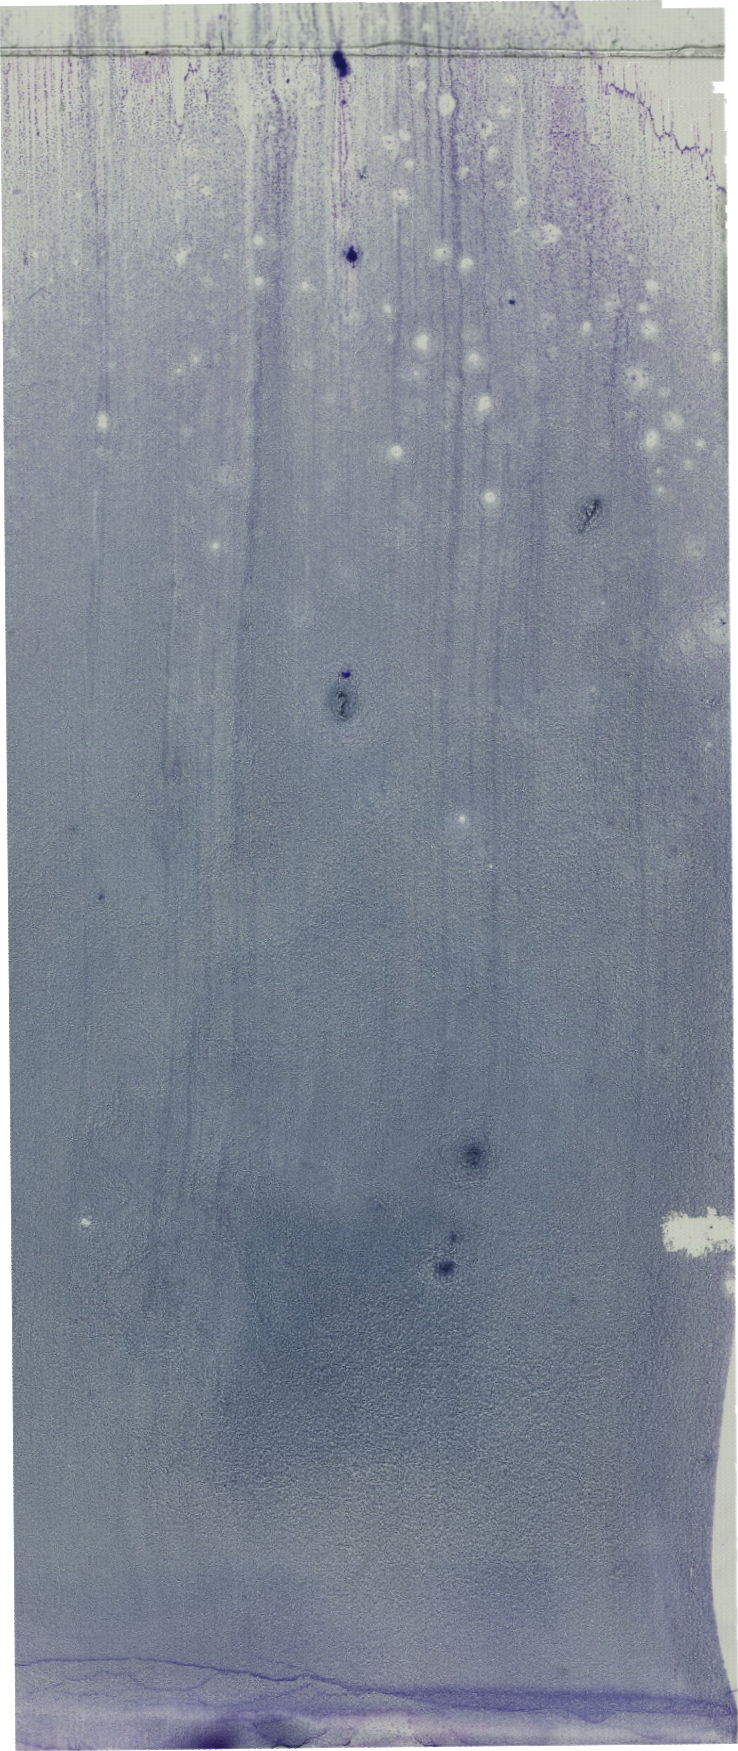
Whole-slide image of a May-Grünwald–Giemsa-stained bone marrow aspirate smear, shown as a low-resolution overview of the whole scanned area (about 20.9 x 49.6 mm). Patient sex: female.
Diagnosis: B Acute Lymphoblastic Leukemia.